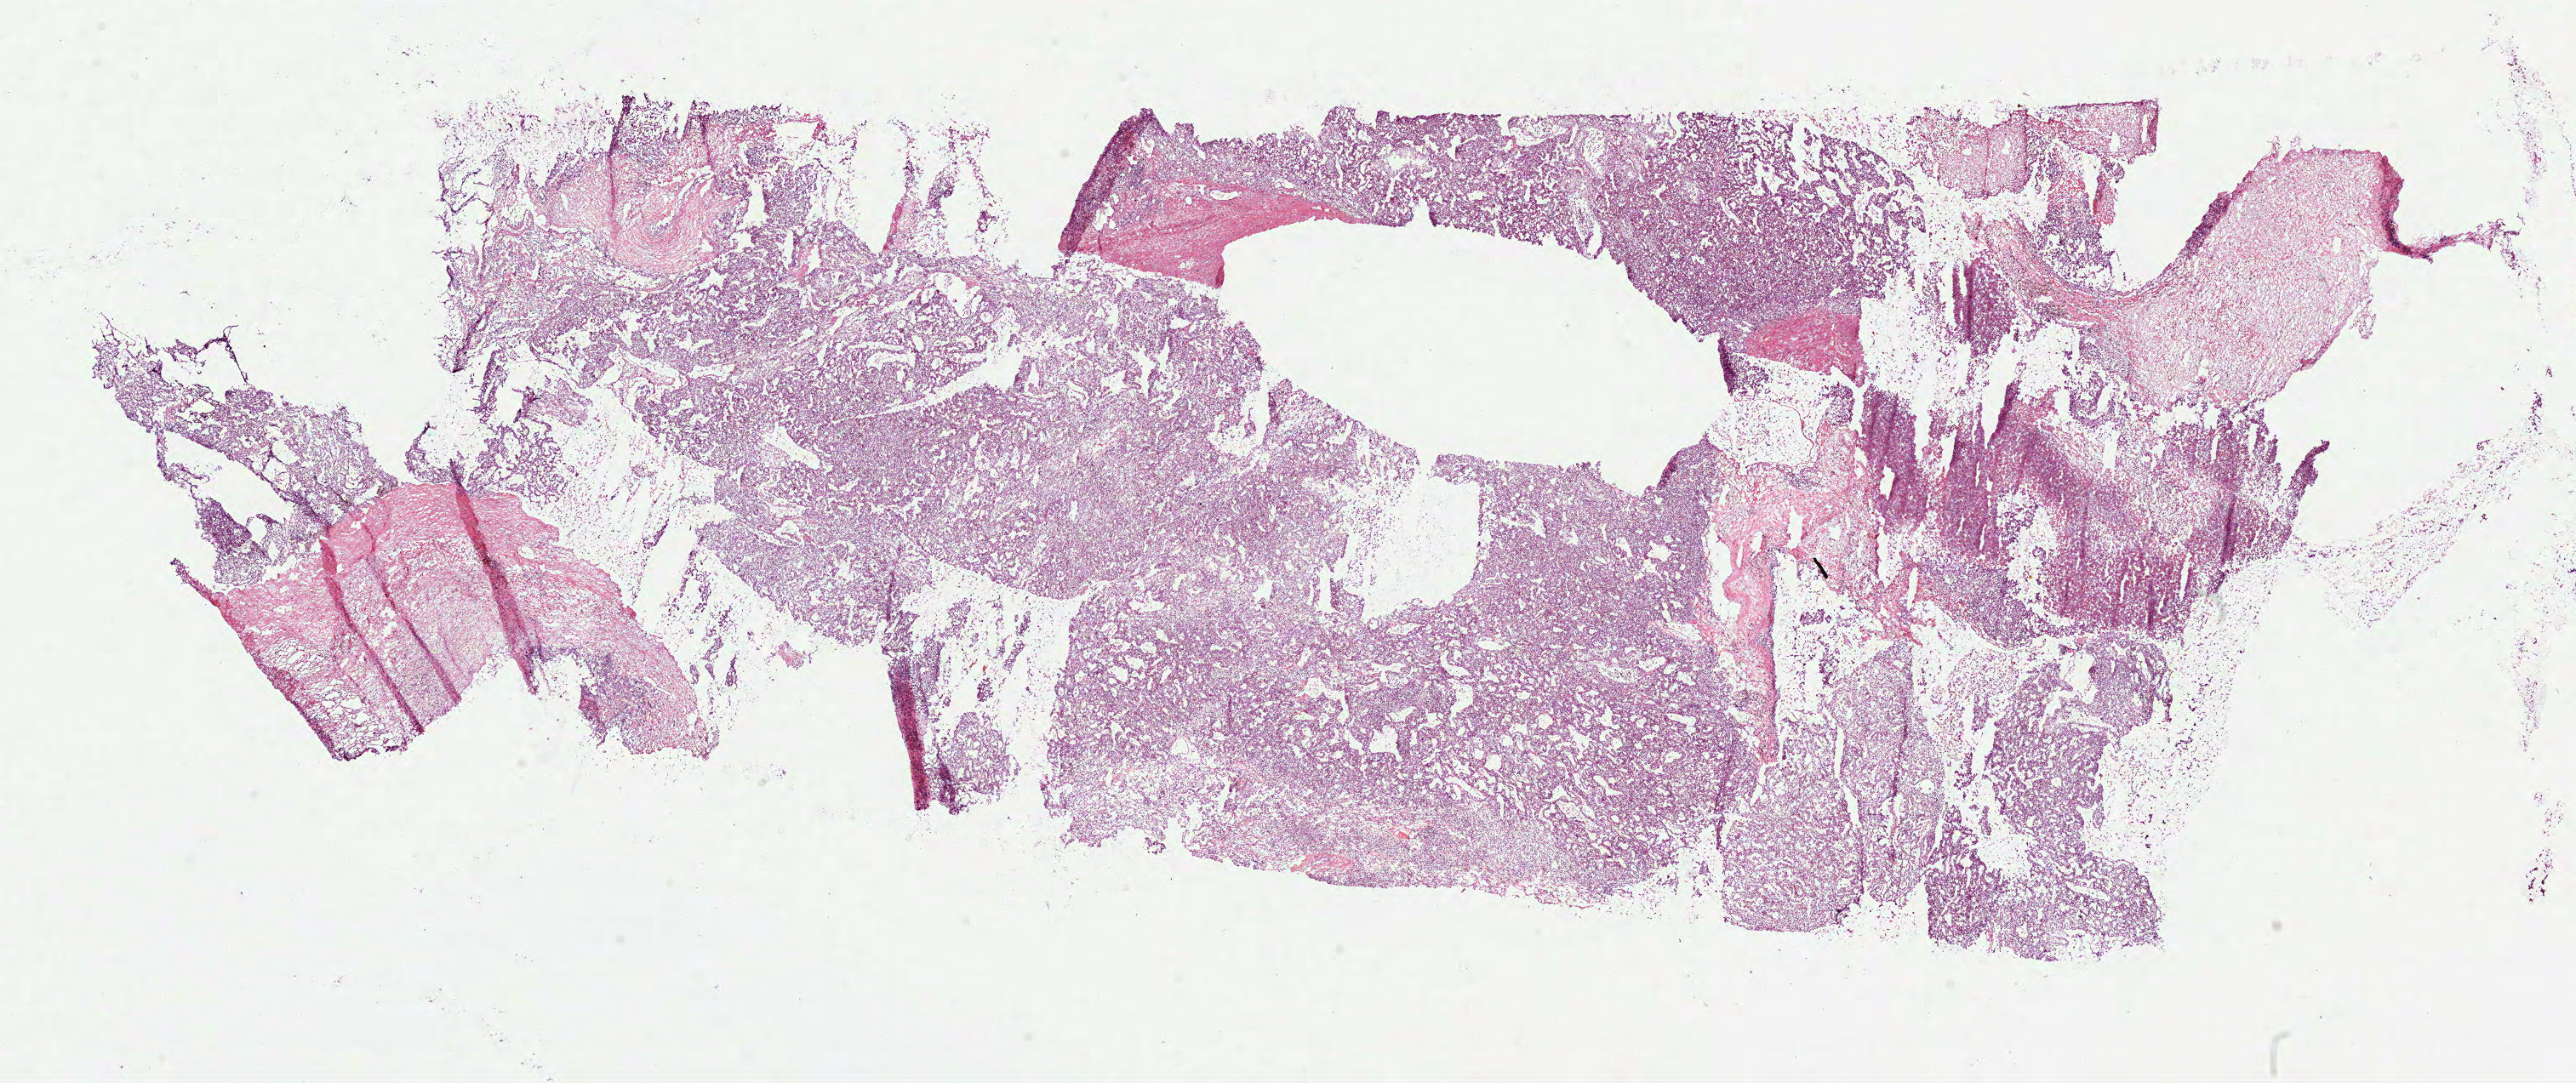
Digitized H&E tissue section (whole slide), low-resolution overview of the scanned area, about 24.4 x 10.3 mm (from a 40x scan); frozen section; sample: primary tumour, kidney. Male, age 65 years at initial diagnosis. Histologic grade: G3 (poorly differentiated). Composition of this section per pathologist review: tumour cells 77%, tumour nuclei 80%, normal cells 0%, stromal cells 15%, necrosis 8%.
AJCC pathologic stage: I (6th edition). TNM: T1a N0 M0. Diagnosis: Clear cell adenocarcinoma, NOS.